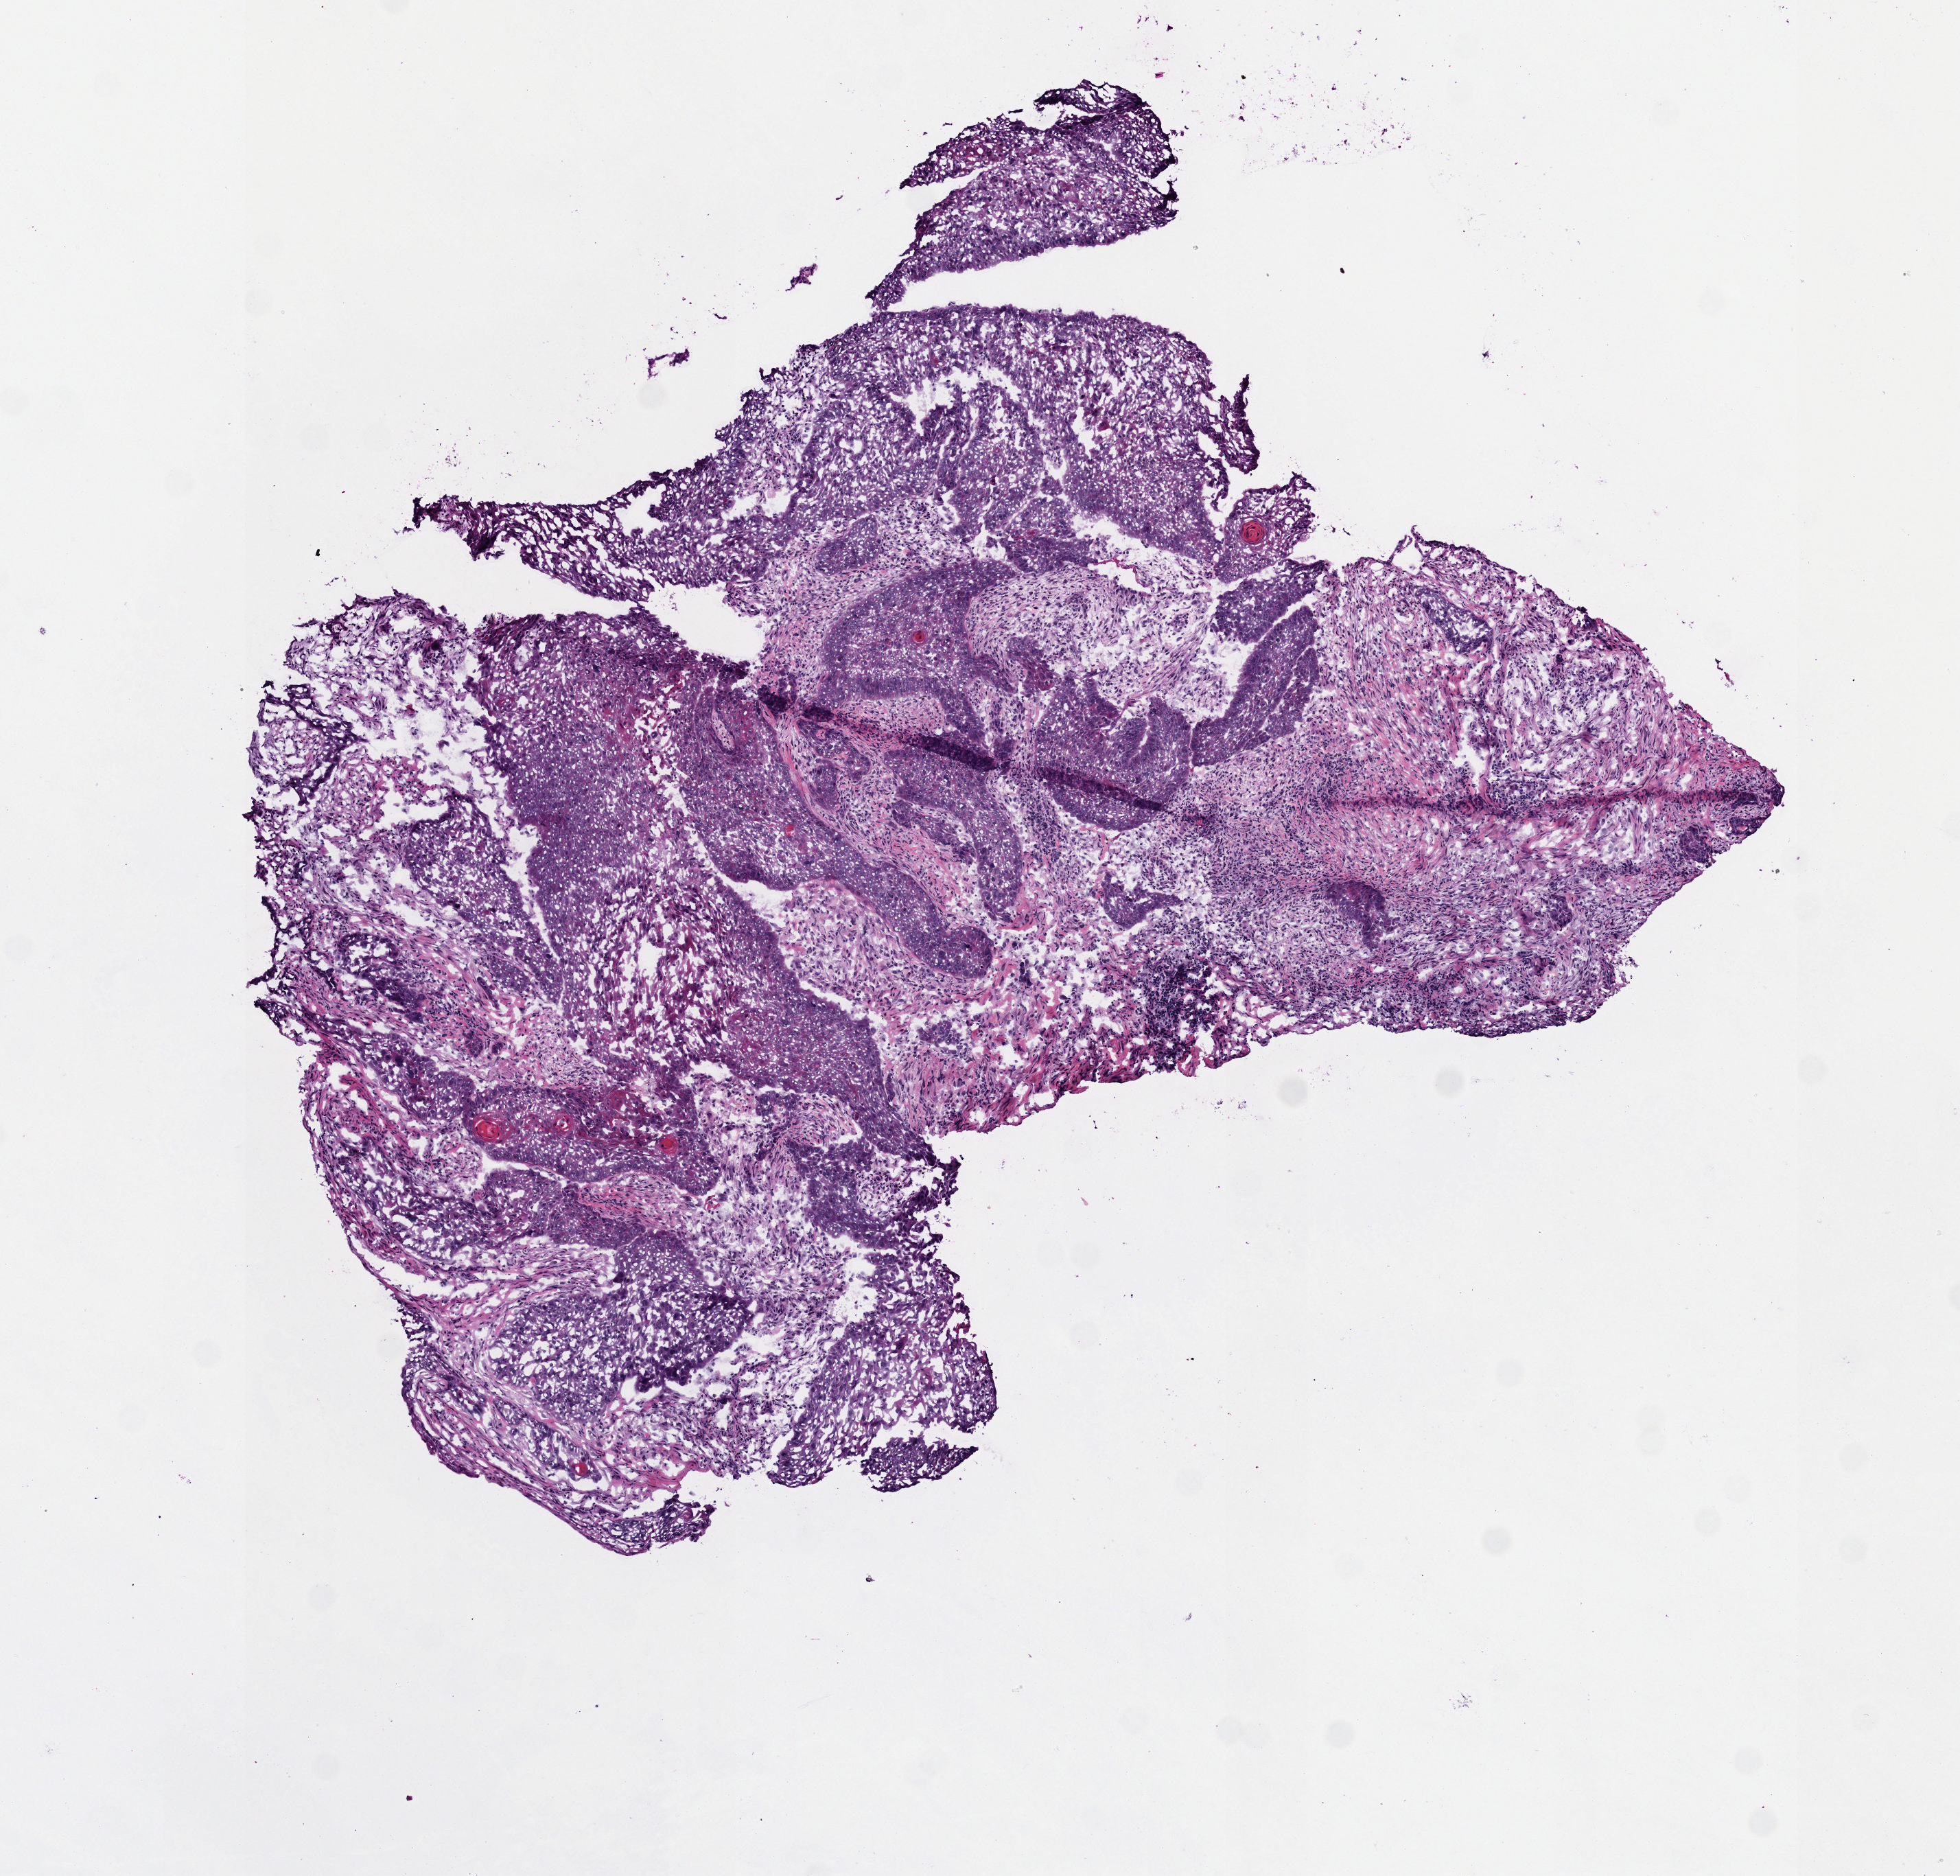
Digitized H&E-stained tissue section (whole slide) — whole scanned area (about 5.6 x 5.4 mm) shown as a low-resolution overview, frozen section from the top of the tissue portion, head and neck, primary tumour sample. Patient: male, age at initial diagnosis 49 years. Histologic grade: G3 (poorly differentiated). Composition of this section per pathologist review: tumour cells 45%, tumour nuclei 65%, normal cells 0%, stromal cells 48%, necrosis 7%. Inflammatory infiltration, as recorded: lymphocyte infiltration 10%, monocyte infiltration 3%, neutrophil infiltration 3%.
AJCC pathologic stage: IVA. Lymph nodes positive (case pathology): 4 of 35 examined. Histologic diagnosis: Squamous cell carcinoma, NOS (tonsil, NOS).